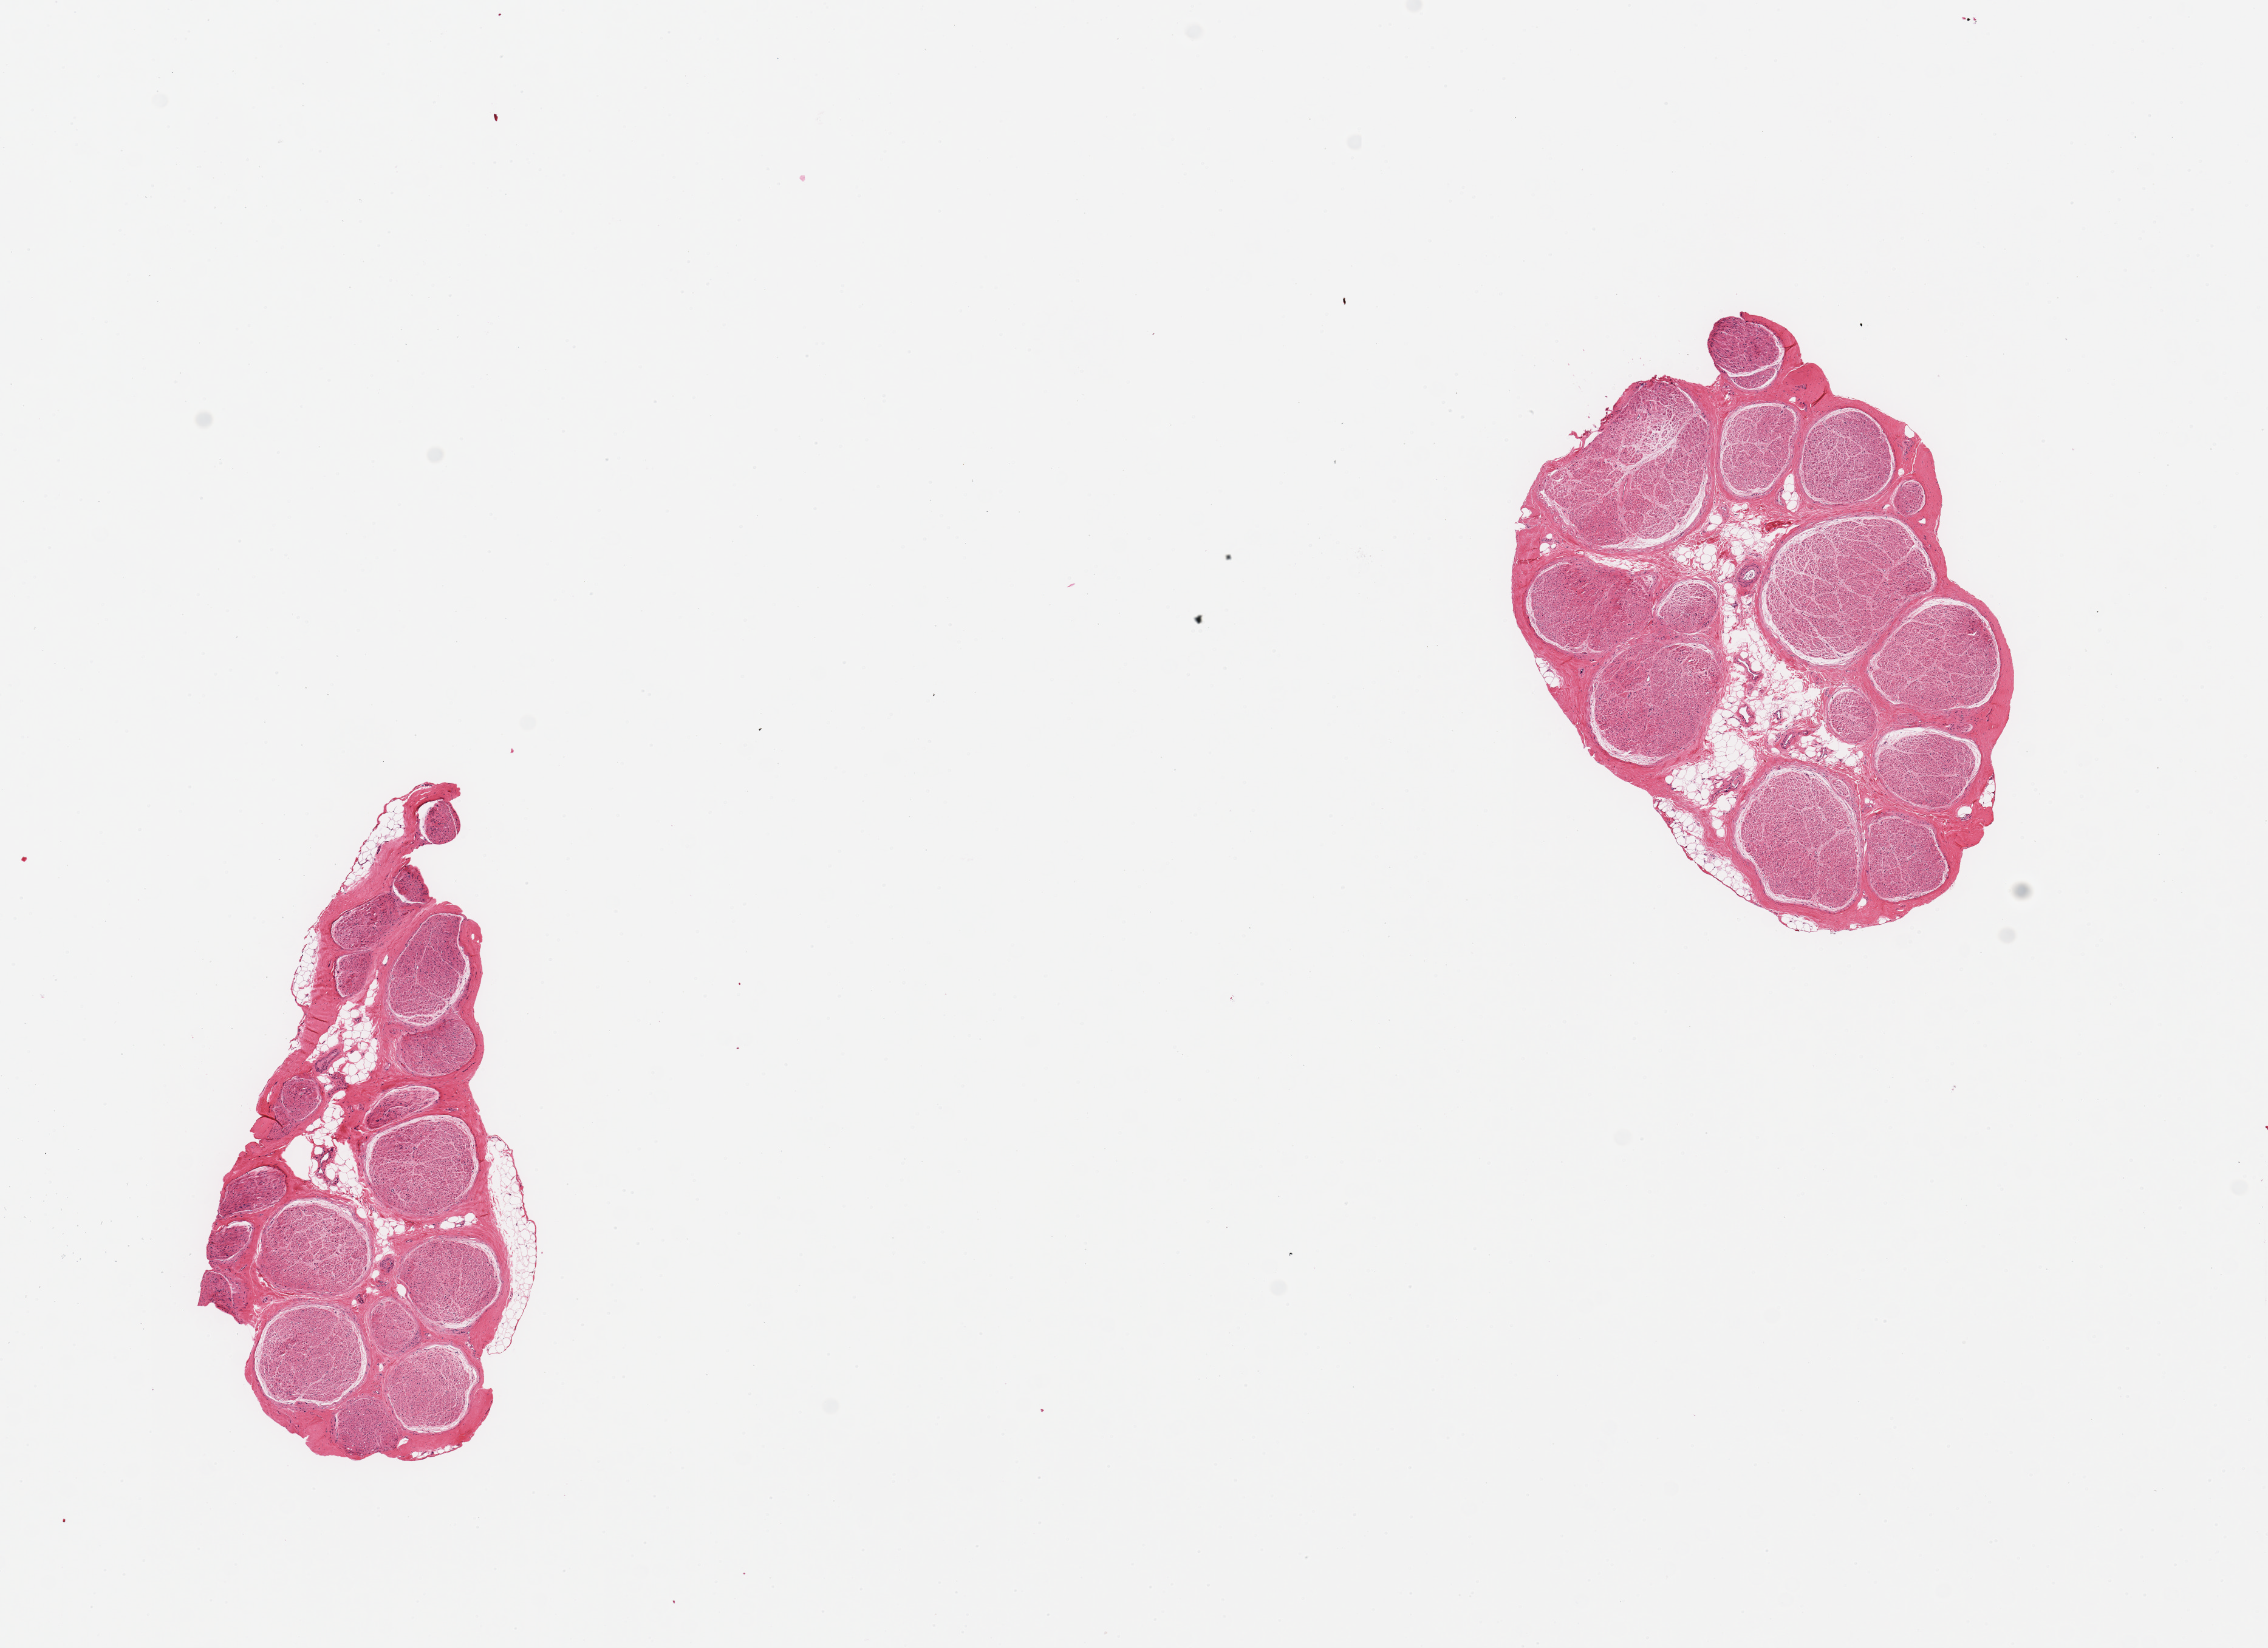
Whole-slide image, H&E stain, shown as a low-resolution overview of the whole scanned area (about 14.8 x 10.7 mm), PAXgene-fixed paraffin-embedded (PFPE) section, section of tibial nerve (target tissue), donor tissue sample. Donor: male.
Pathologist's review note for this sample: 2 pieces; 10% internal fat.